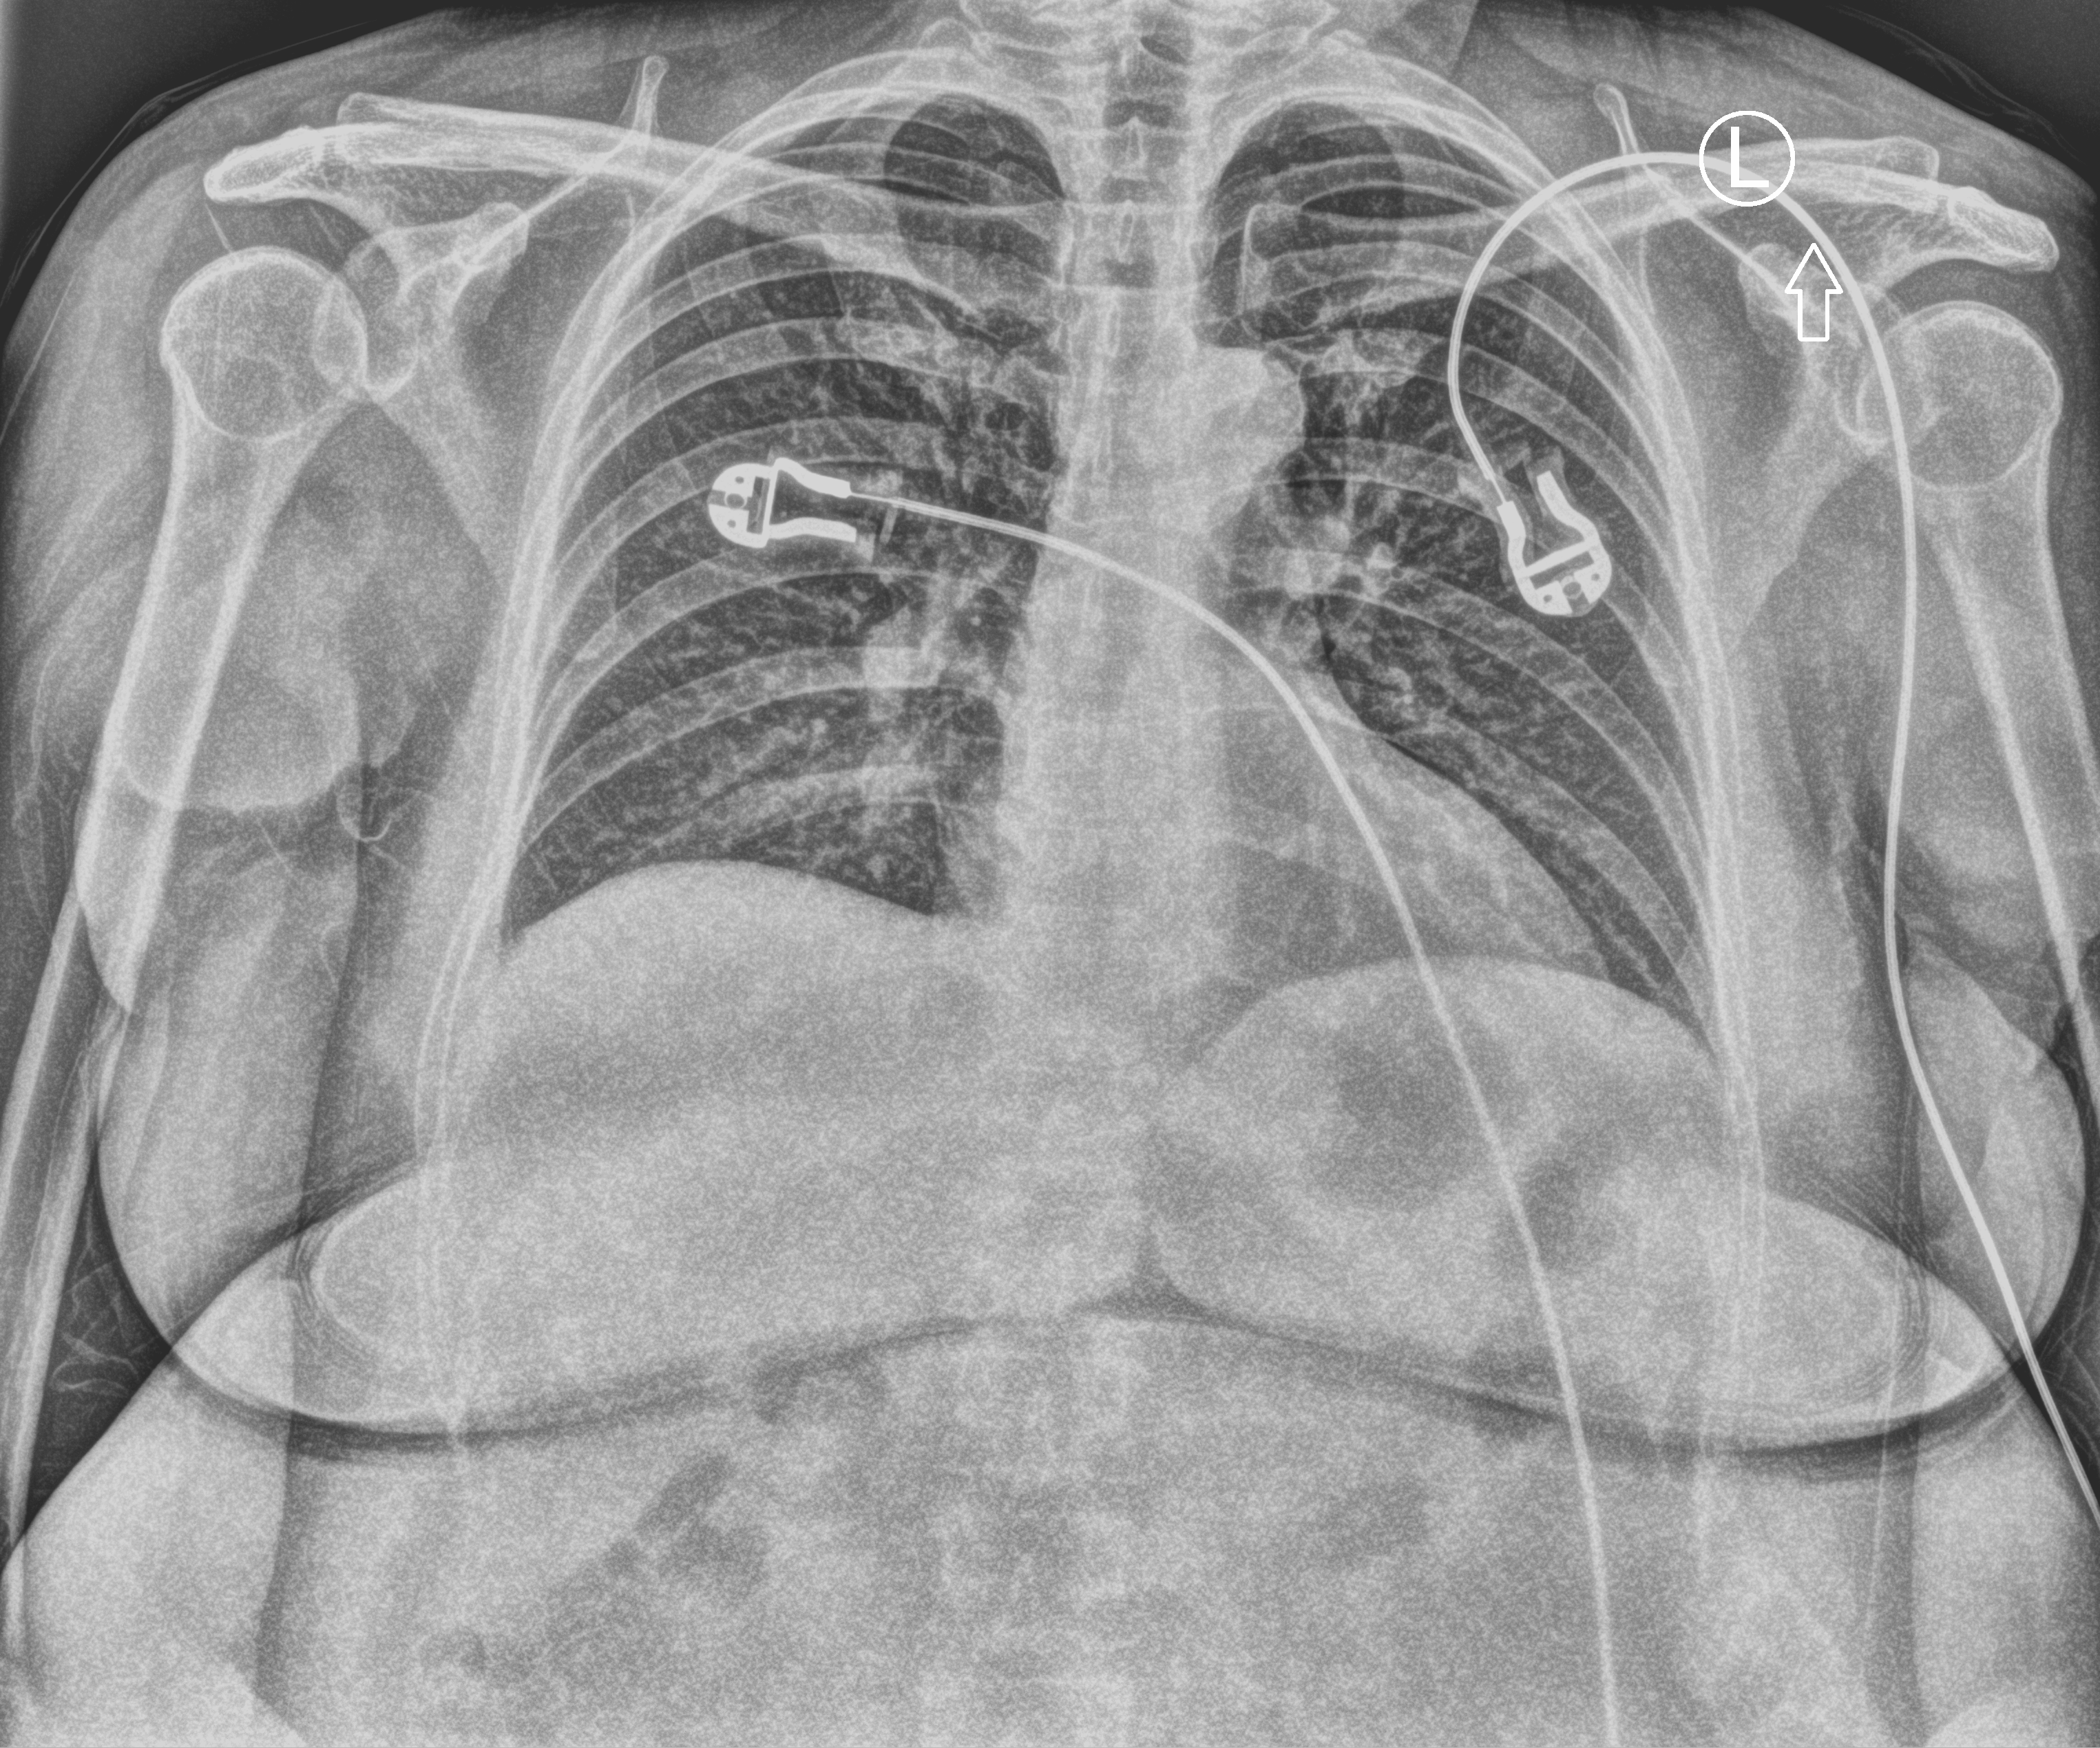
Portable chest radiograph, anteroposterior (AP) projection. Female patient hospitalised with COVID-19, age 18–59 years.
Admission-level facts for this patient (not findings on this image; timing relative to this image not recorded): mechanically ventilated during this hospital stay: no; length of hospital stay: 1 day.